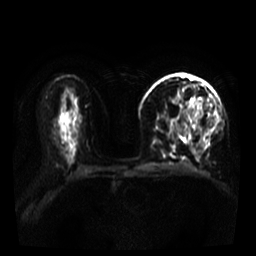
Breast MRI, one axial slice; position 20 of 39 along the scan axis; diffusion-weighted series; image 2 of 4 stored at this slice position (different b-values; order by instance number); 3 T; 5 mm slice thickness; 256 × 256 image matrix. Female patient.
Outlined on this slice (expert manual segmentation):
- tumour on diffusion-weighted imaging: bounding box <172,99,203,118> (left, top, right, bottom; pixels)